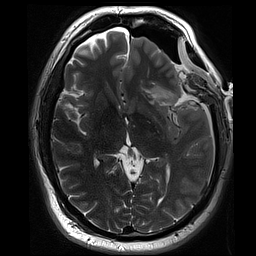
Brain MRI from a brain-tumour surgery series, one axial slice. Position 45 of 70 along the scan axis. 2 mm slice thickness. 256 × 256 image matrix, field of view 220 × 220 mm. From the clinical record (not read from this slice): histopathology: Oligodendroglioma; WHO grade: 3; IDH mutation: yes; tumour location: Left Sylvian Fissure (Temporal).
Outlined on this slice (outlined manually by an expert reader):
- residual tumour: box from (x=148, y=87) to (x=178, y=106) px